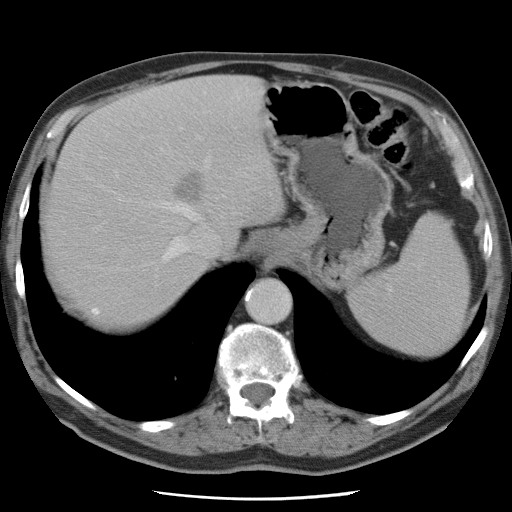
Contrast-enhanced abdominal CT, one axial slice; position 61 of 78 along the scan axis; 120 kVp; intravenous contrast given; soft-tissue window (W 400 / L 40 HU); 512 × 512 image matrix. Male patient, age 75 years. Case-level facts recorded for this patient, not image findings: diagnosis: colorectal cancer liver metastases, imaged before liver resection; multiple liver metastases: yes; largest metastasis: 2.4 cm; chemotherapy before resection: yes.
Outlined on this slice (expert manual segmentation):
- hepatic veins: bounding box (x1, y1, x2, y2) in pixels: (117, 94, 239, 262)
- liver: (45, 78, 277, 324)
- planned liver remnant (the part of the liver to remain after resection): (46, 135, 202, 325)
- portal vein (with intrahepatic branches): (114, 172, 116, 174)
- liver metastasis: (94, 309, 99, 314)
- liver metastasis: (174, 171, 205, 203)